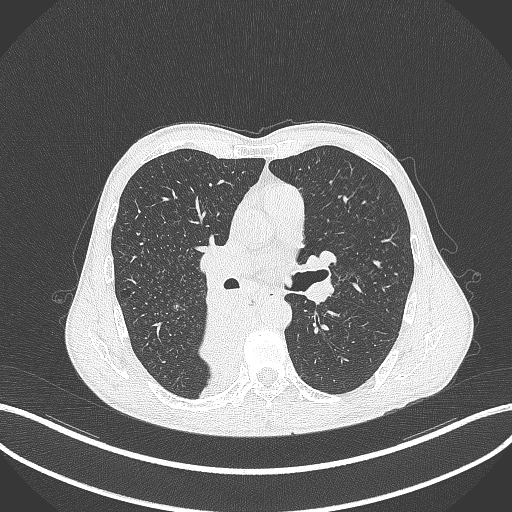
Chest CT, one axial slice. Position 215 of 371 along the scan axis. Reconstruction kernel B70f. Lung window (W 1500 / L -600 HU). 512 × 512 image matrix, field of view 400 × 400 mm. Male patient, age 58 years. From the clinical record (not read from this slice): clinical TNM (as recorded): T3 N1 M1.
Outlined on this slice (rectangle marked by the reading radiologist):
- lung tumour (recorded histology: squamous cell carcinoma): bounding box <198,295,246,380> (left, top, right, bottom; pixels)